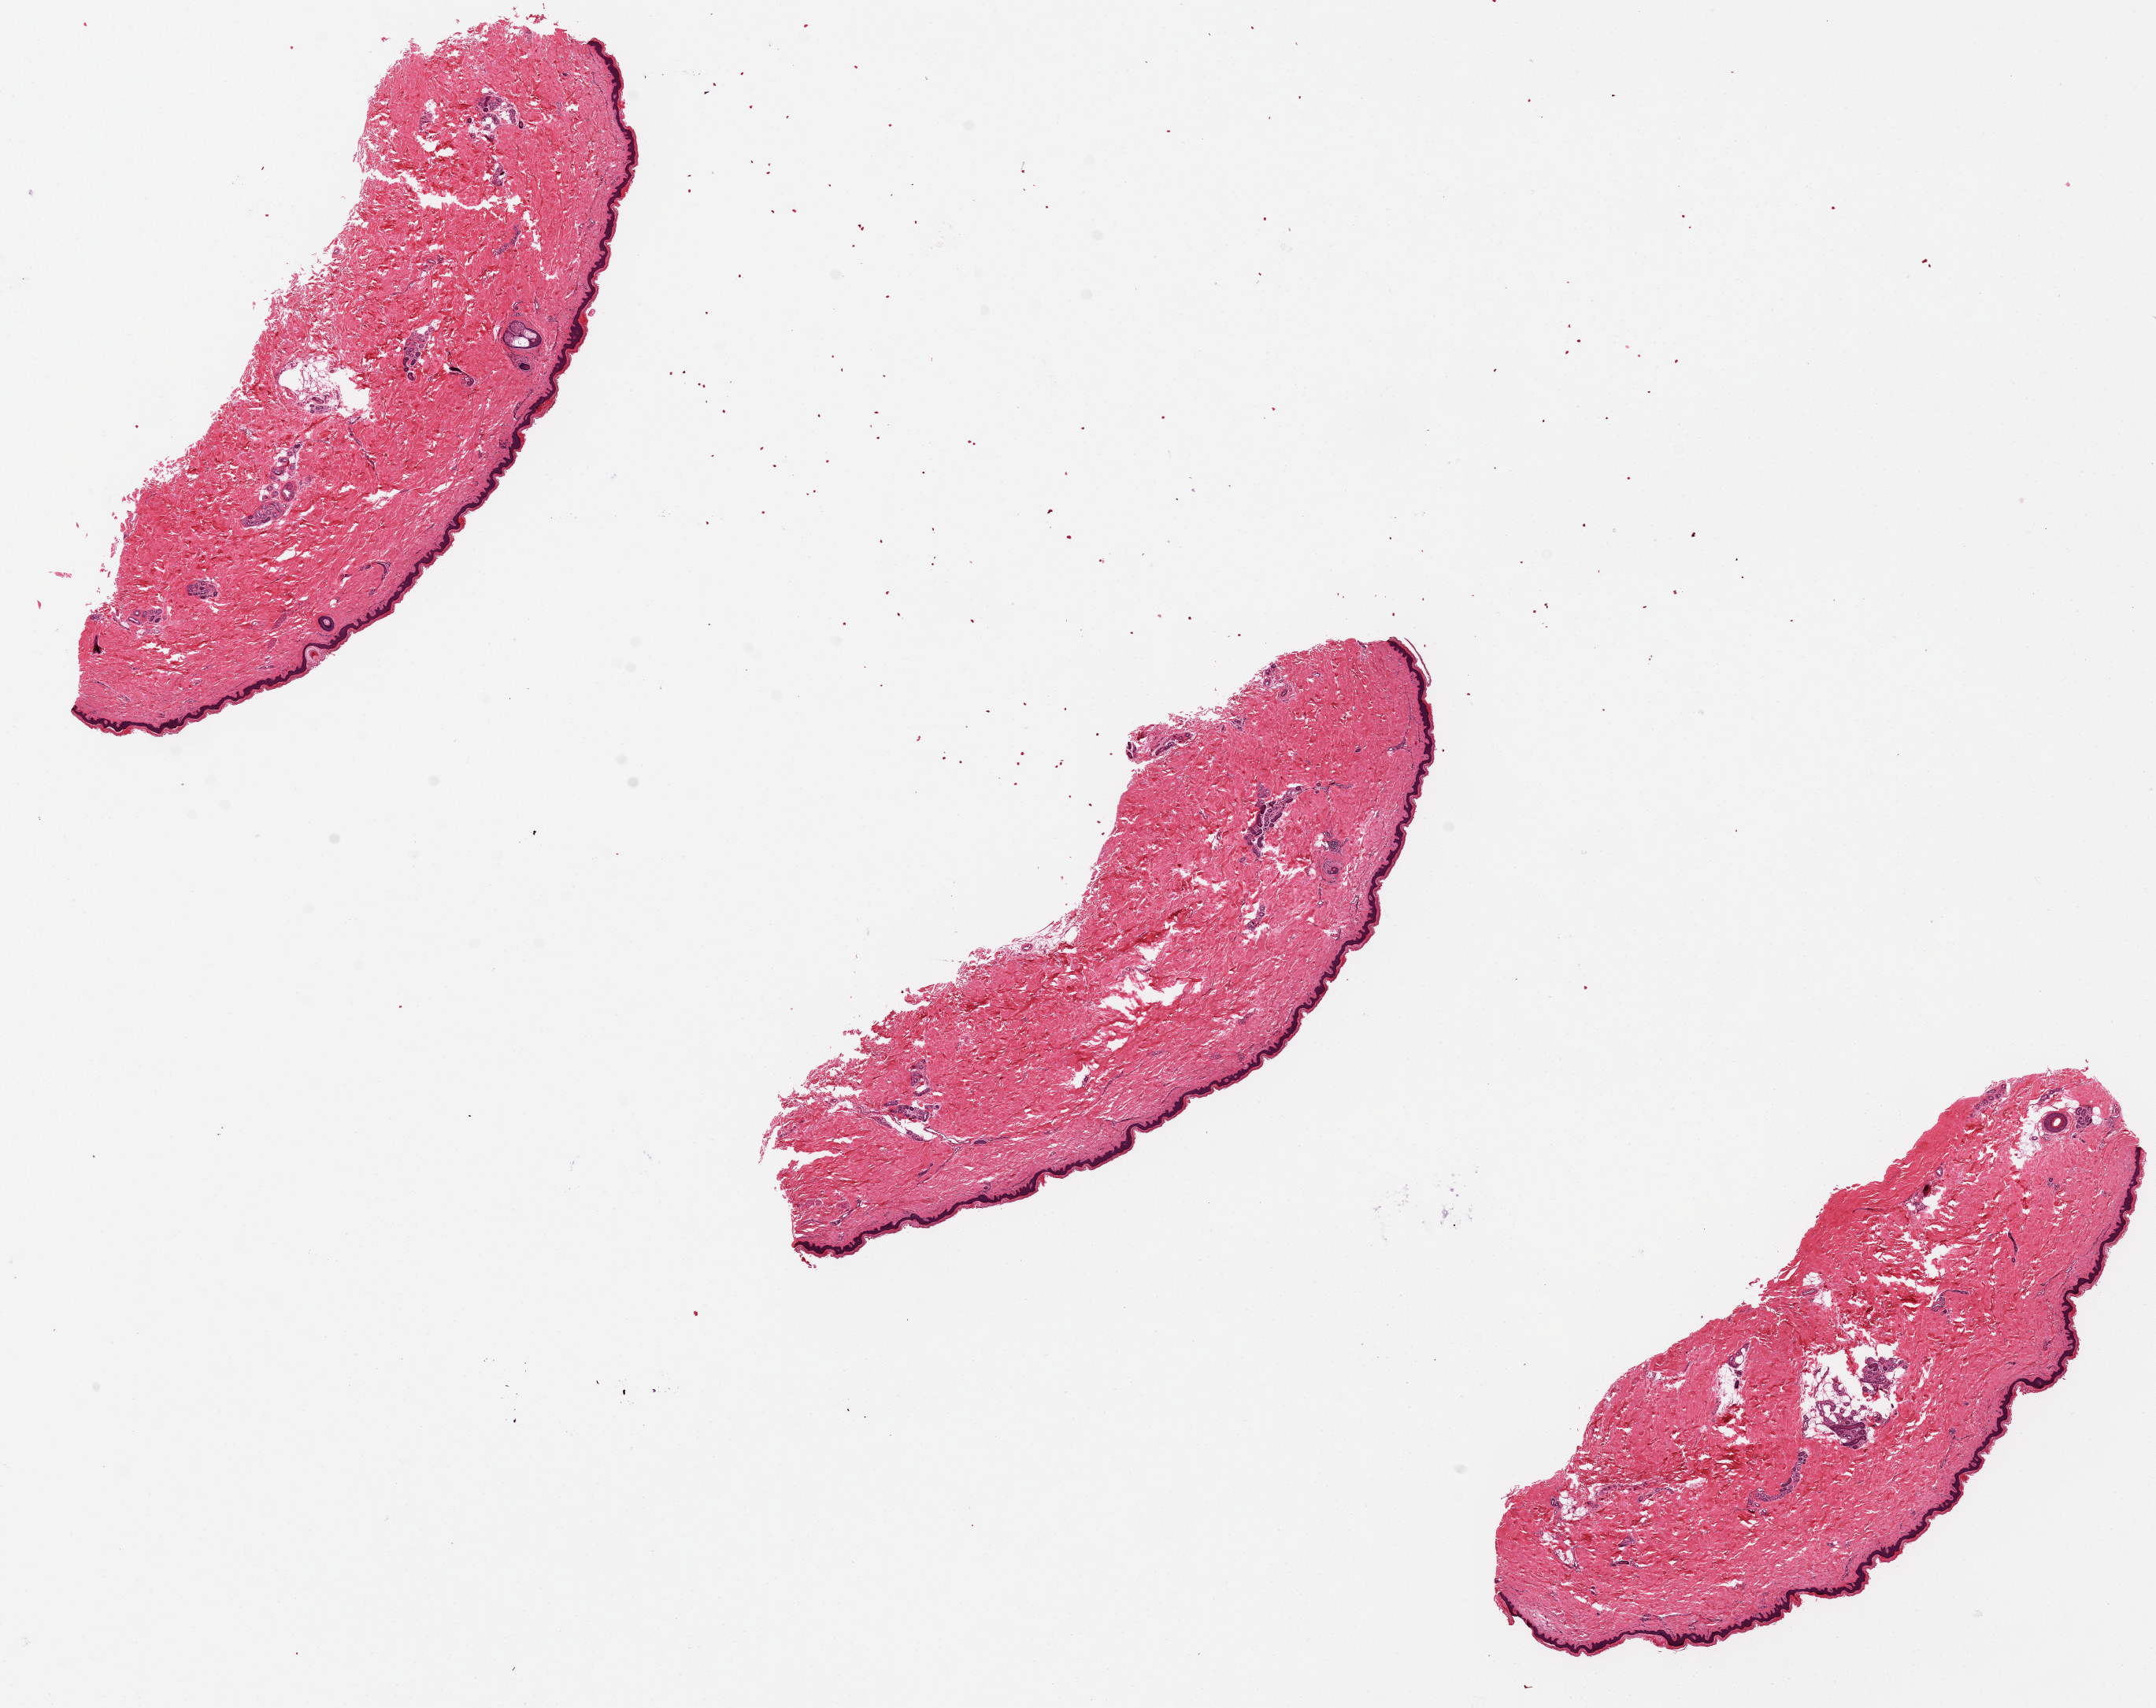
Haematoxylin and eosin whole-slide image — whole scanned area (about 21.7 x 17.2 mm) shown as a low-resolution overview. PAXgene-fixed paraffin-embedded (PFPE) section. Target tissue: skin of lower leg. Donor tissue sample.
Pathologist's review note for this sample: Epidermis is ~2% of specimen thickness.